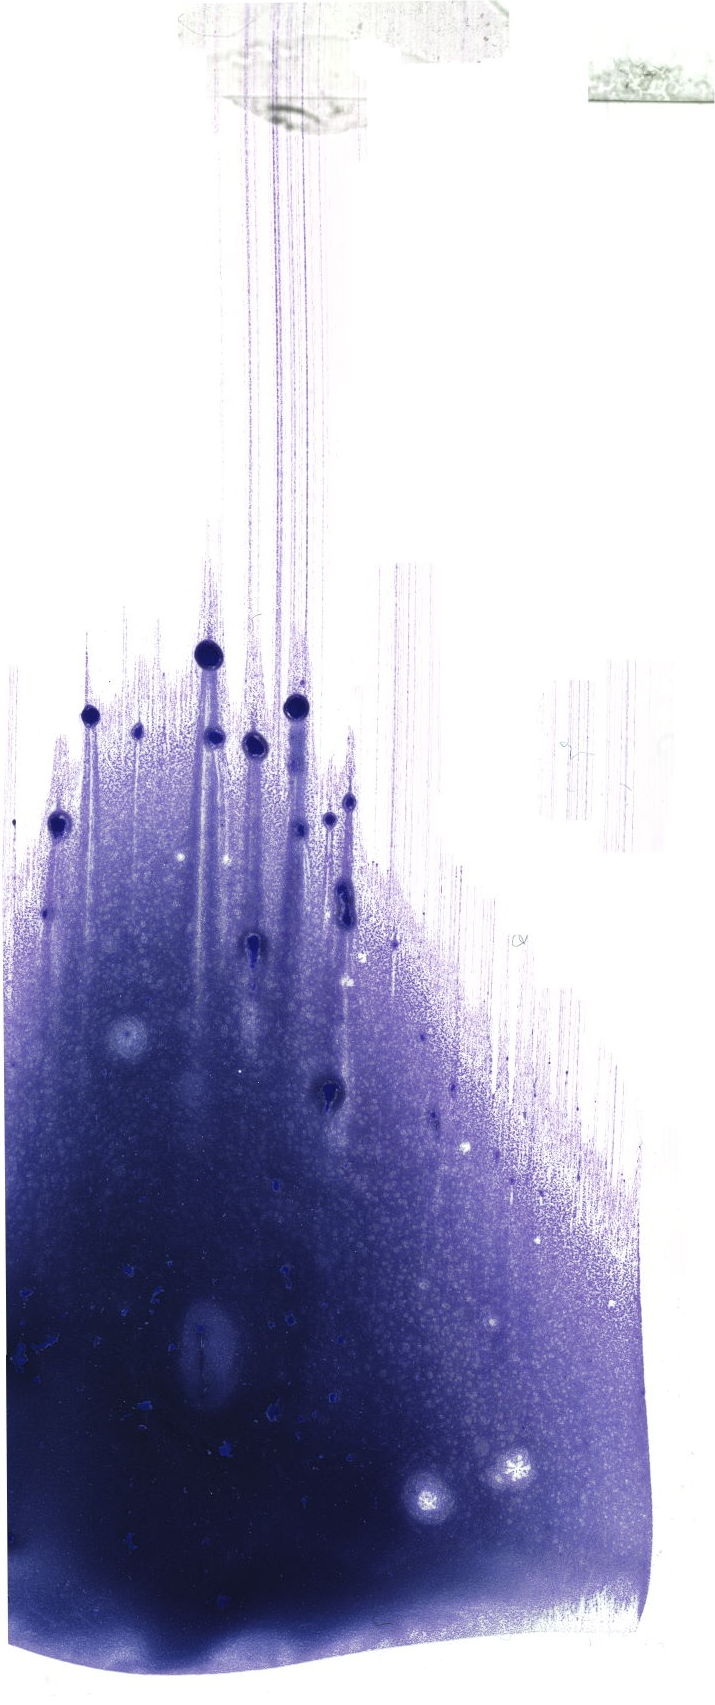
May-Grünwald–Giemsa-stained marrow aspirate smear (whole slide), low-resolution overview of the scanned area, about 20.3 x 48.3 mm. Patient sex: male.
* diagnosis: Chronic Phase Chronic Myeloid Leukemia, BCR-ABL1 Positive